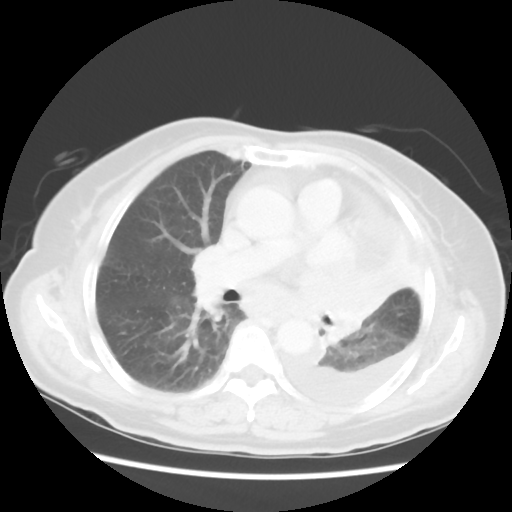
Chest CT, one axial slice; slice 31 of 52 in the series (ordered by position); lung window (W 1500 / L -600 HU); 5 mm slice thickness; 512 × 512 image matrix, field of view 336 × 336 mm. Female patient, age 72 years. Case-level facts recorded for this patient, not image findings: clinical TNM (as recorded): T4 N3 M1b.
Structures marked on this image (rectangle marked by the reading radiologist):
- lung tumour (recorded histology: large cell carcinoma): bounding box [x1, y1, x2, y2] px = [301, 255, 389, 345]